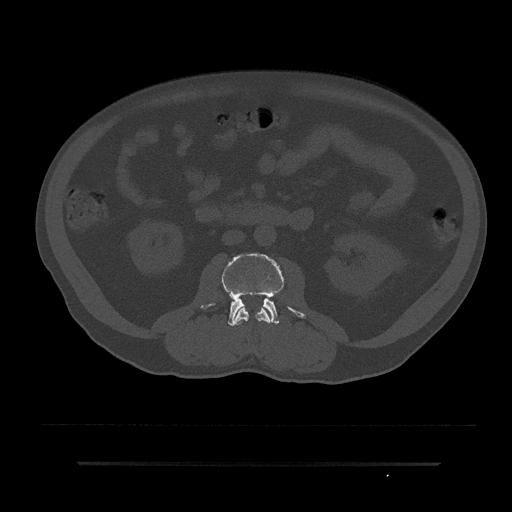
CT including the spine, one axial slice. Slice 30 of 797 in the series (ordered by position). Reconstruction kernel Br40s/3. 120 kVp. Bone window (W 1800 / L 400 HU). 512 × 512 image matrix, field of view 464 × 464 mm. Male patient, age 59 years. From the clinical record (not read from this slice): primary cancer: bile ducts.
Outlined on this slice (semi-automatically segmented with operator editing):
- L2 vertebra: bounding box (x1, y1, x2, y2) in pixels: (233, 305, 272, 325)
- L3 vertebra: (202, 254, 305, 326)